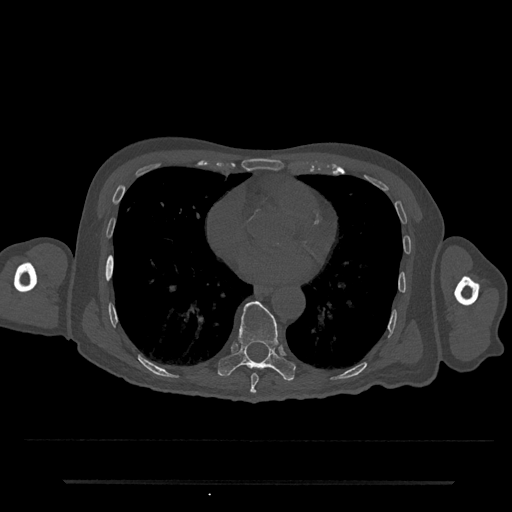
CT including the spine, one axial slice. Reconstruction kernel Br40s/3. Bone window (W 1800 / L 400 HU). 0.5 mm slice thickness. 512 × 512 image matrix, field of view 427 × 427 mm. Patient: male, 74 years. From the clinical record (not read from this slice): primary cancer: prostate.
Structures marked on this image (semi-automatically segmented with operator editing):
- T8 vertebra: box from (x=250, y=373) to (x=259, y=394) px
- T9 vertebra: (x=218, y=301)–(x=295, y=381)